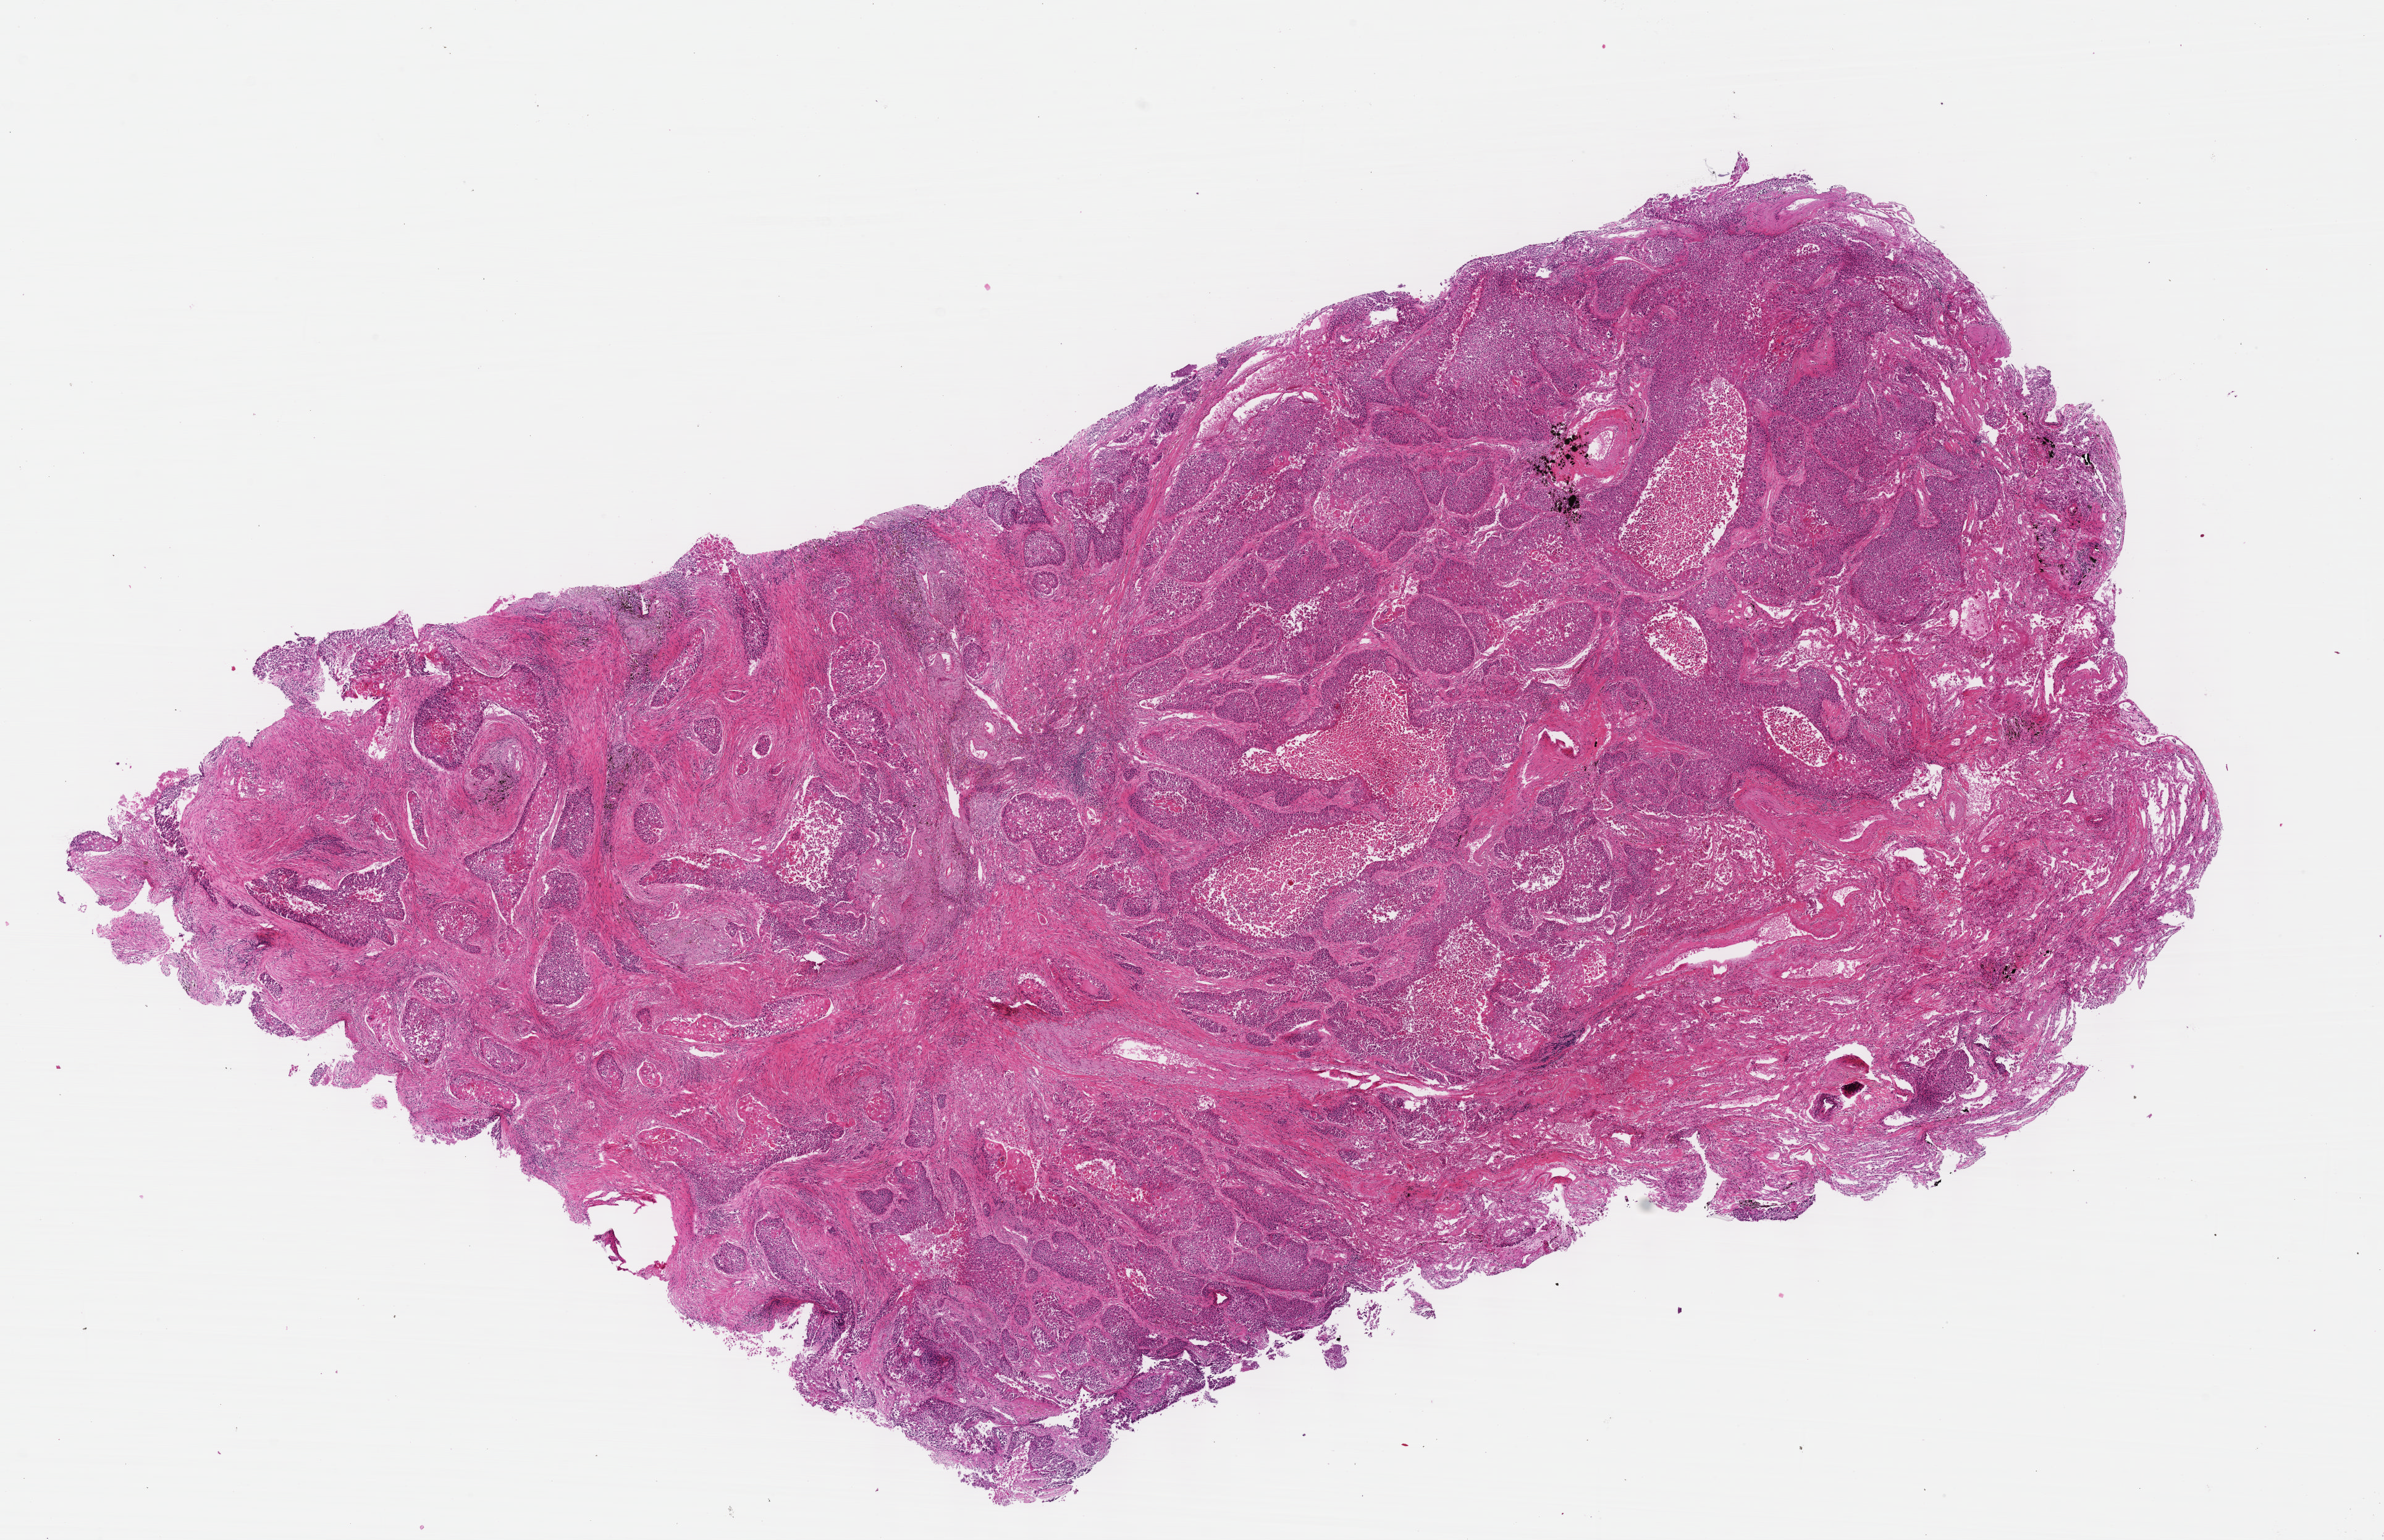
H&E whole-slide image, shown as a low-resolution overview of the whole scanned area (about 15.6 x 10.1 mm, acquisition: 40x scan). Formalin-fixed paraffin-embedded (FFPE) diagnostic section. Lung, primary tumour sample. Male patient; age at initial diagnosis 55 years.
• AJCC pathologic stage: IA (5th edition)
• diagnosis: Squamous cell carcinoma, NOS (lower lobe, lung)